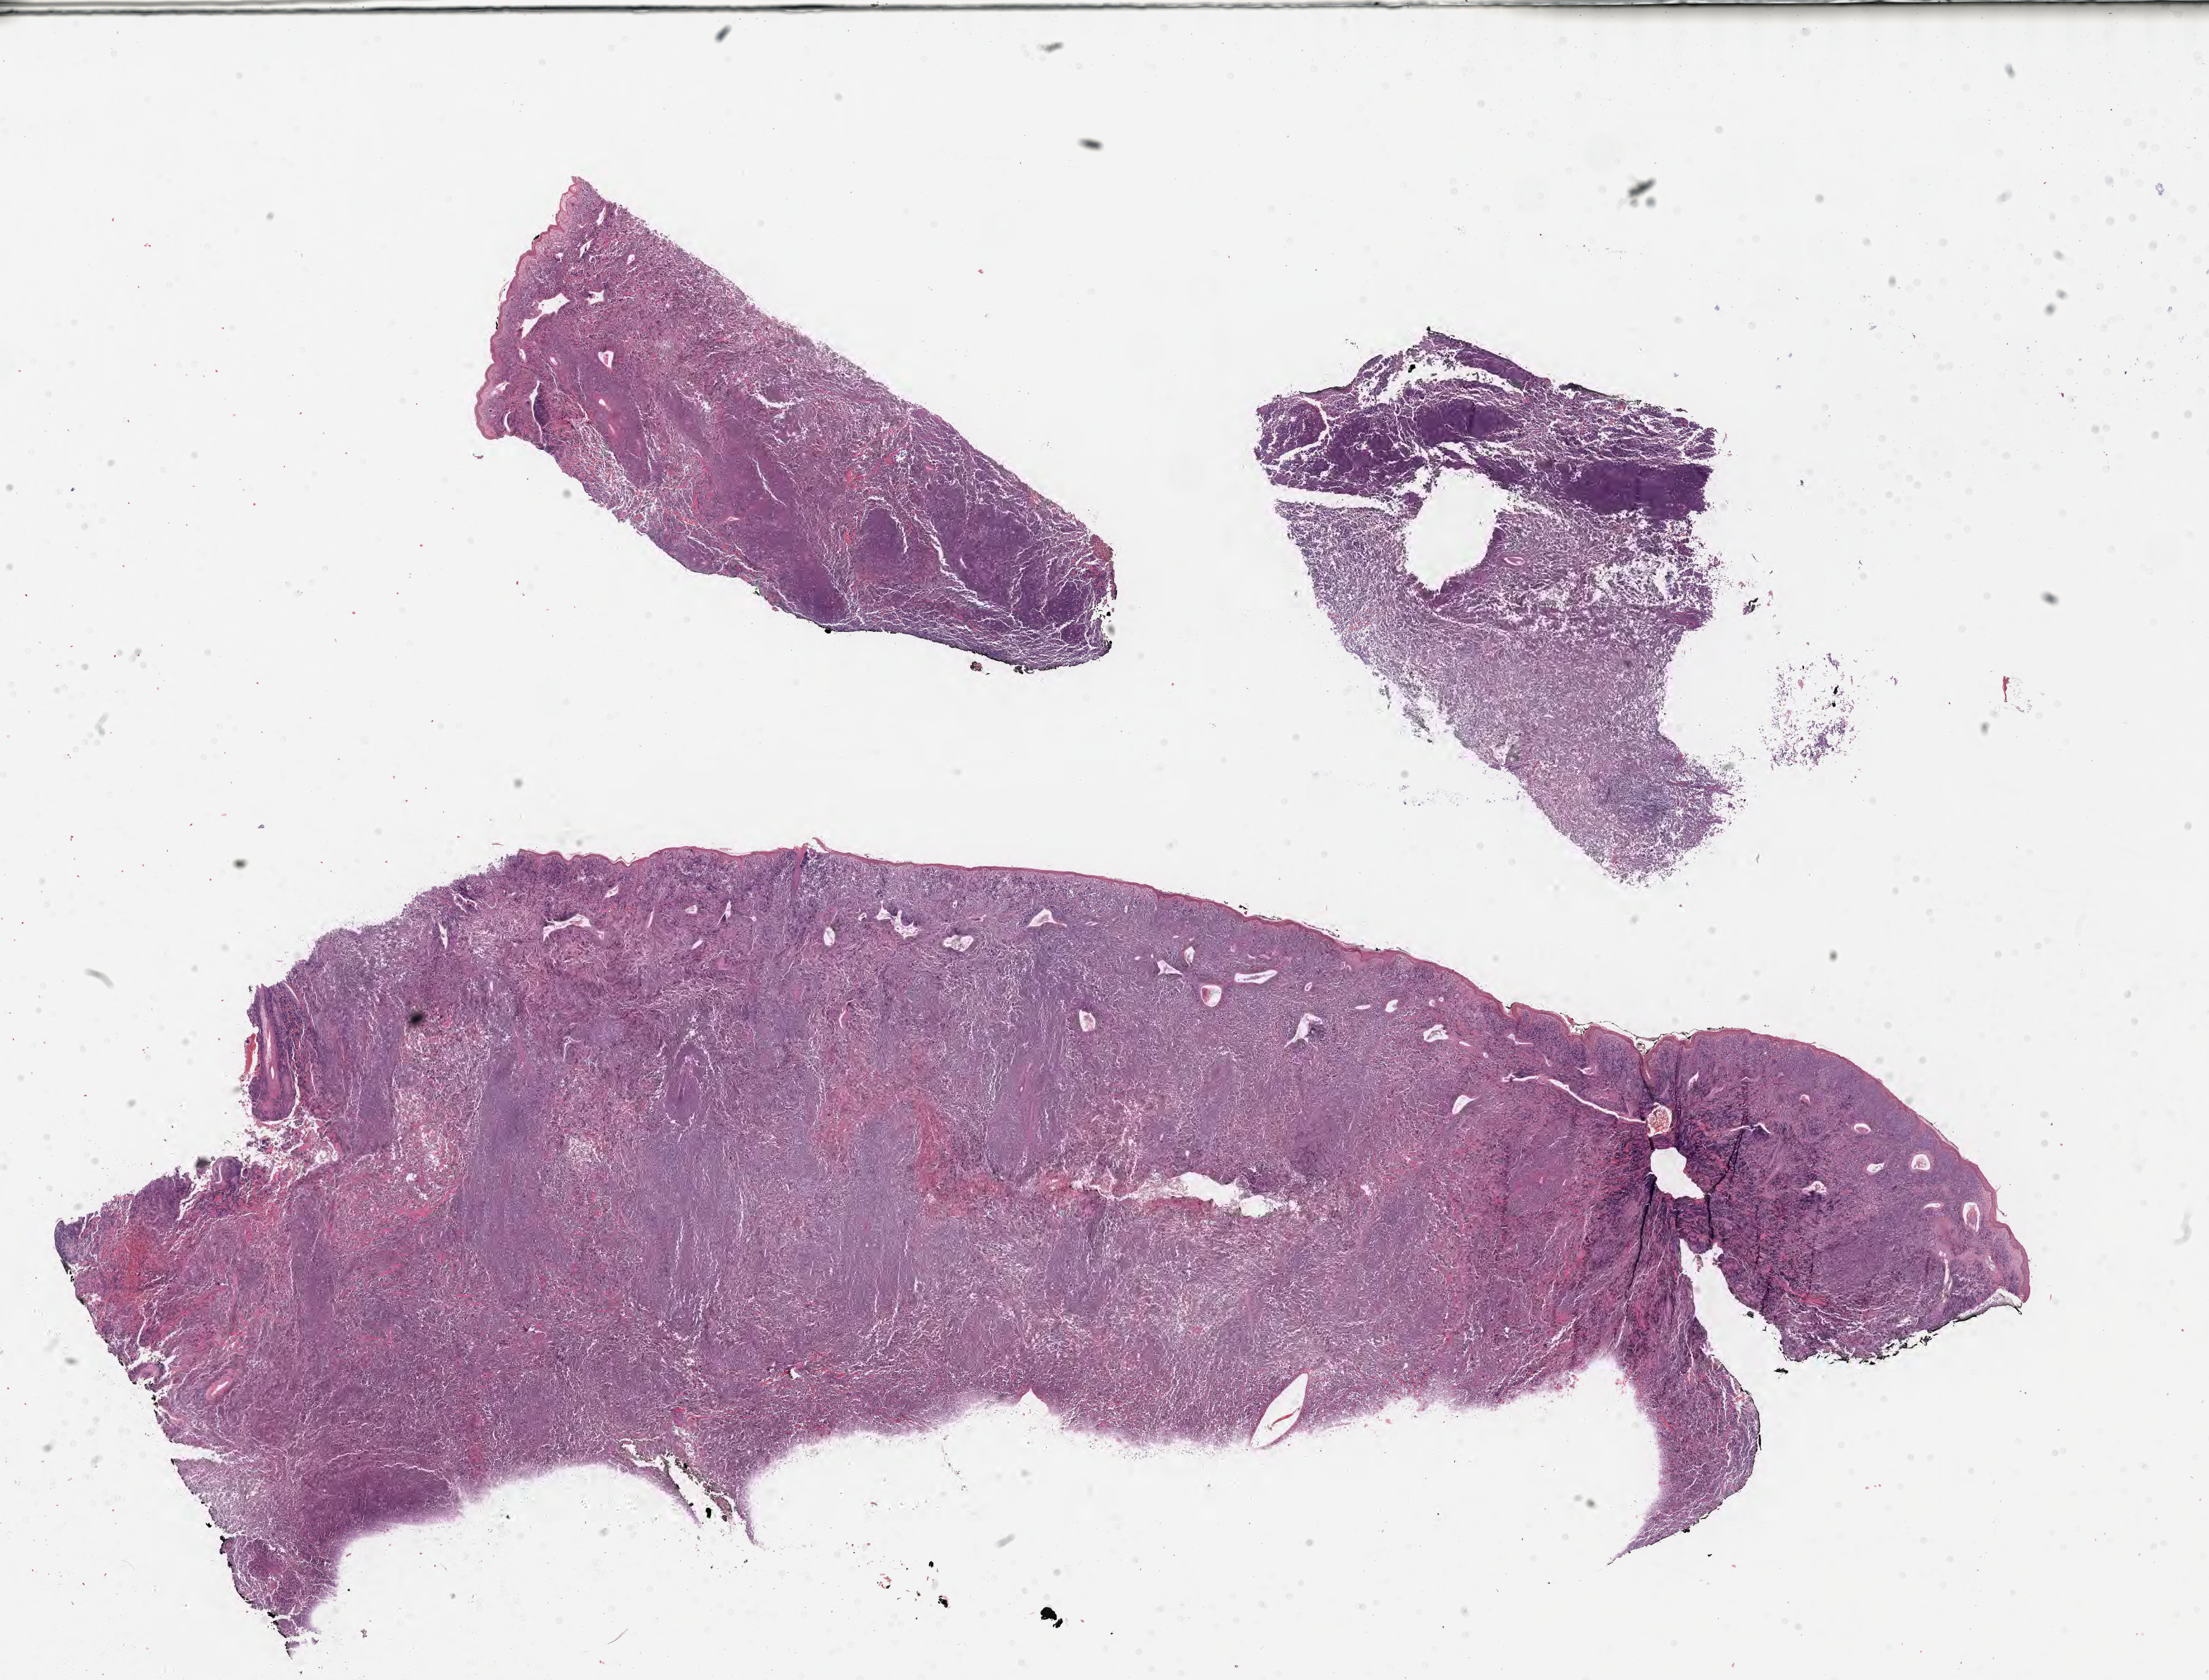
Whole-slide image, haematoxylin and eosin stain, low-resolution overview of the scanned area, about 28.2 x 21.4 mm, specimen: tumor tissue. Male patient, aged 46.
• histologic diagnosis: Burkitt lymphoma, NOS